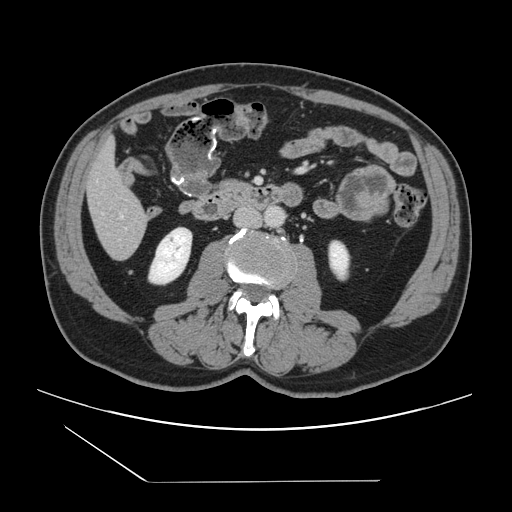
Contrast-enhanced abdominal CT, one axial slice; position 32 of 157 along the scan axis; 120 kVp; intravenous contrast given; soft-tissue window (W 400 / L 40 HU); 2.5 mm slice thickness; 512 × 512 image matrix. Male patient, age 61 years. From the clinical record (not read from this slice): diagnosis: colorectal cancer liver metastases, imaged before liver resection; multiple liver metastases: yes; largest metastasis: 5.5 cm; disease in both lobes: yes.
Annotated regions visible in this slice (outlined manually by an expert reader):
- hepatic veins: box from (x=121, y=215) to (x=123, y=217) px
- liver: (x=87, y=144)–(x=148, y=259)
- planned liver remnant (the part of the liver to remain after resection): (x=86, y=143)–(x=143, y=219)